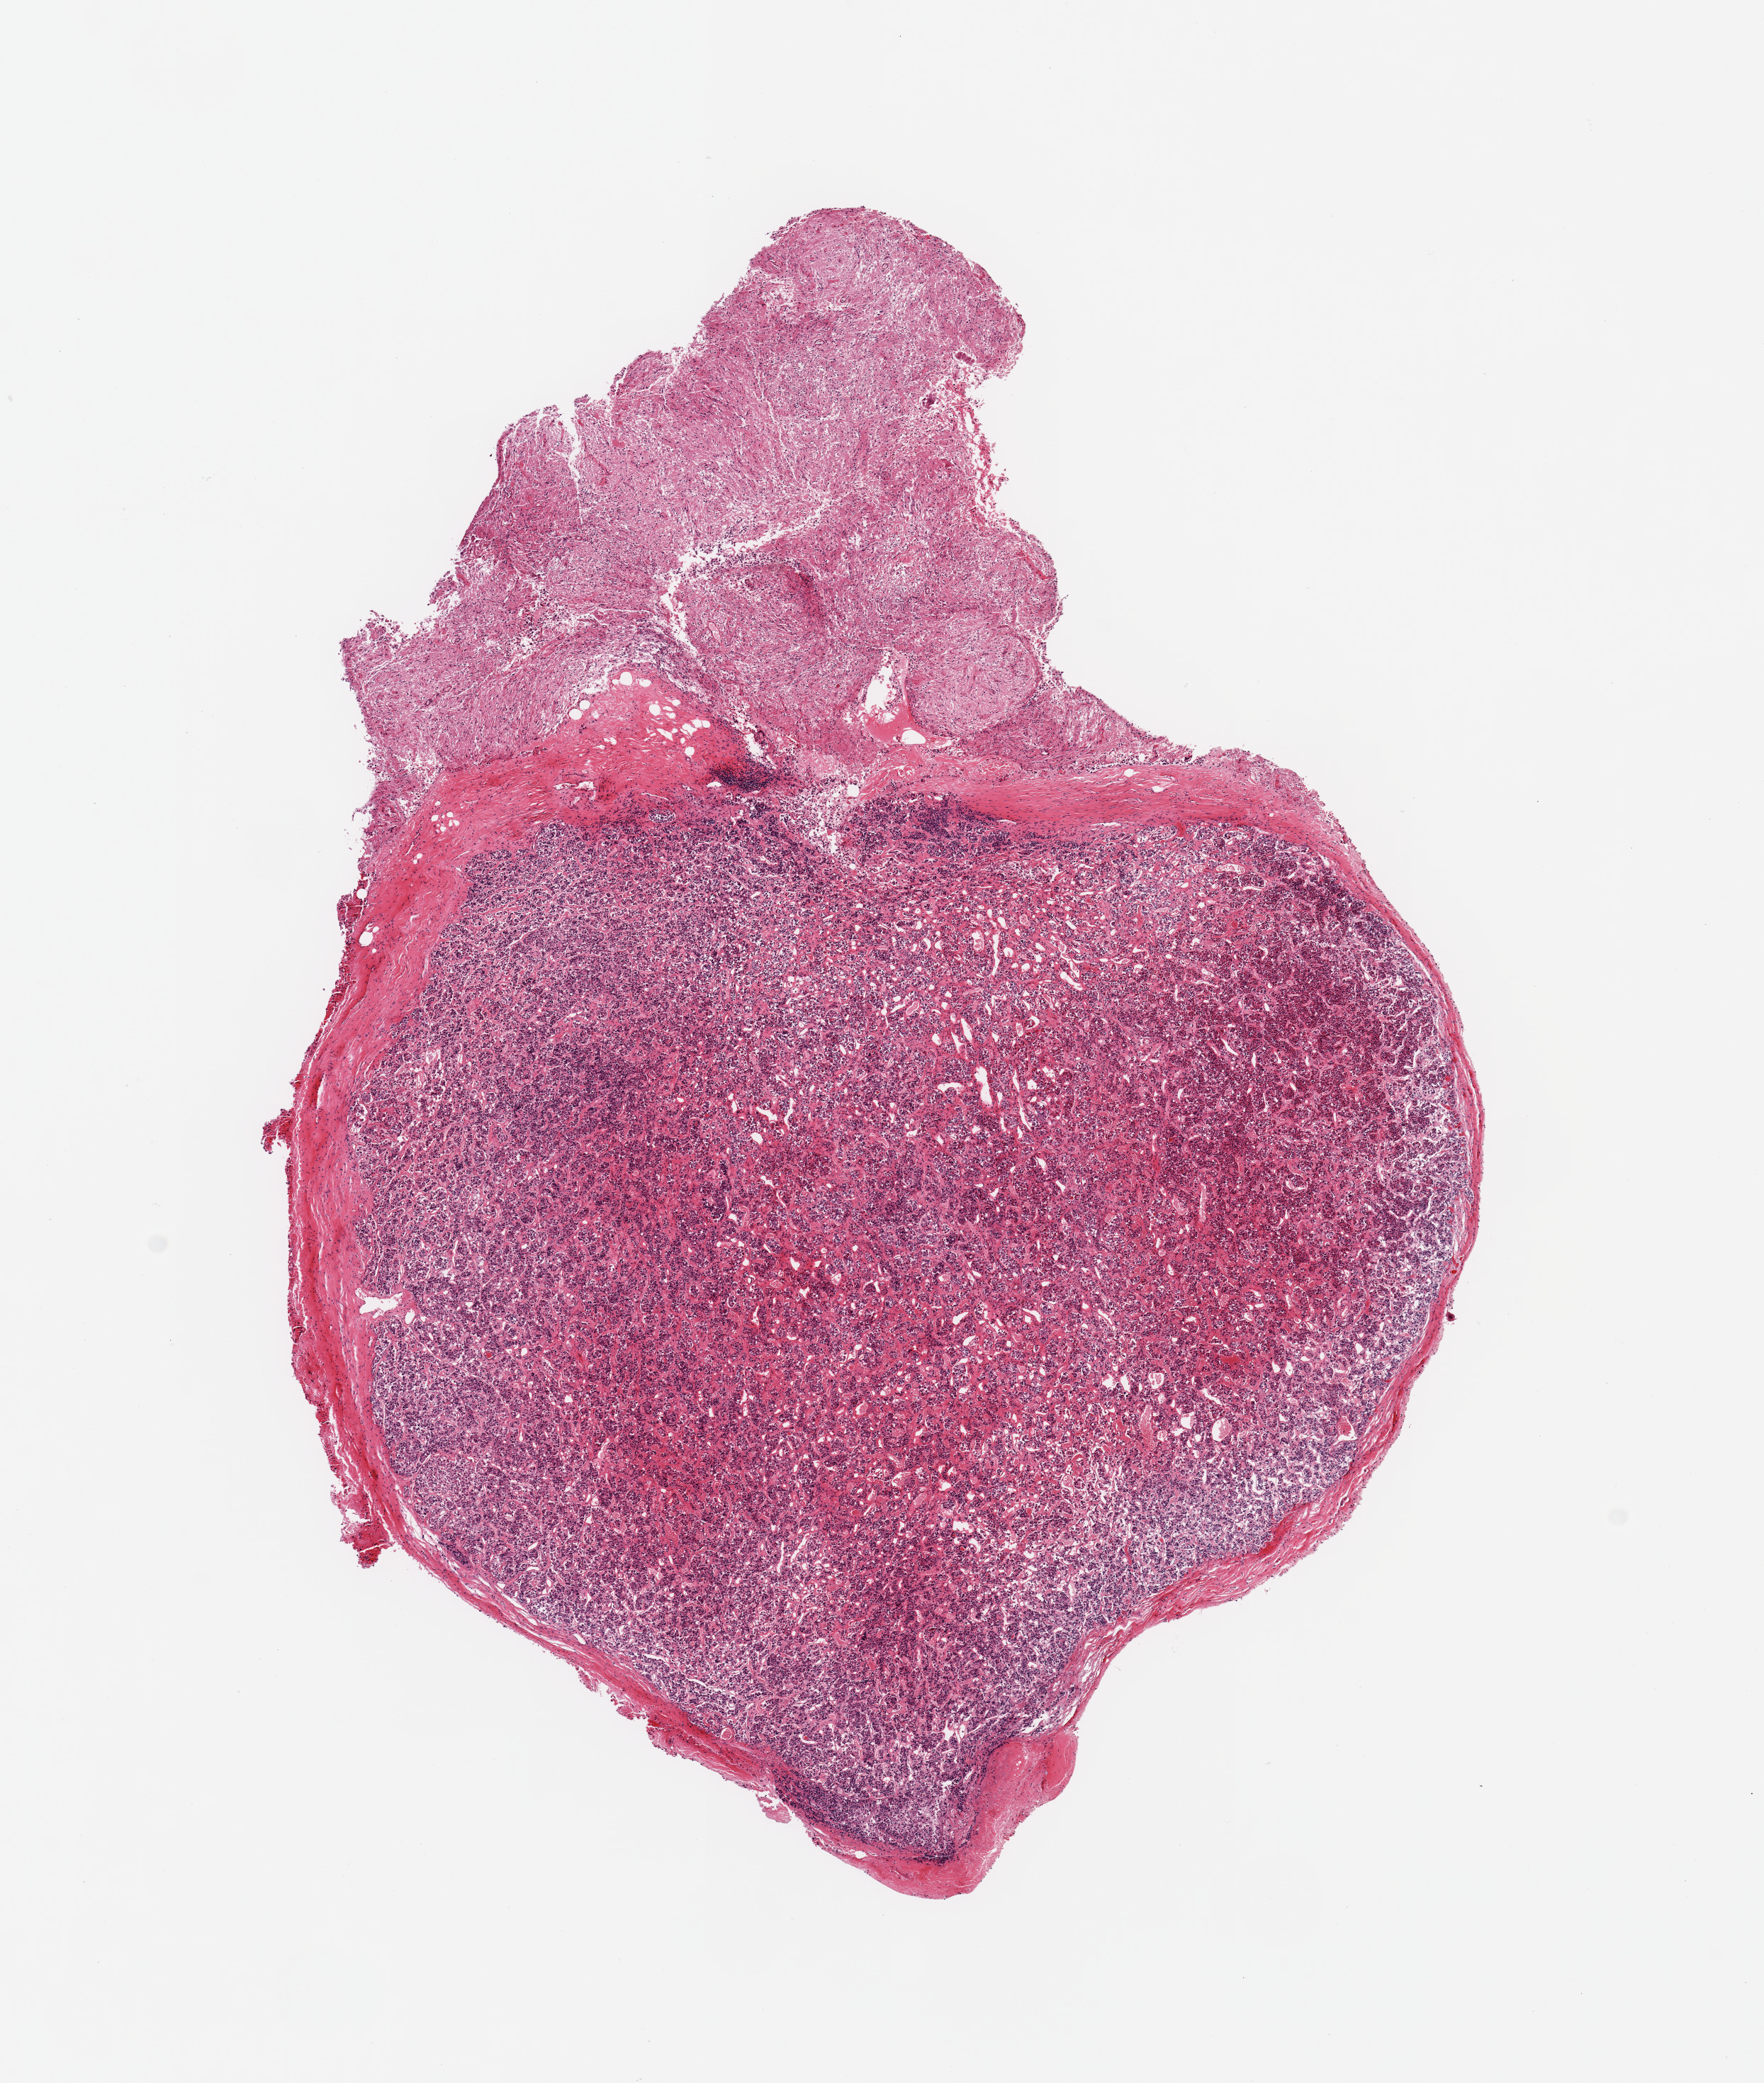
Digitized hematoxylin and eosin (H&E)-stained section, shown as a low-resolution overview of the whole scanned area (about 9.8 x 11.6 mm, slide scanned at 20x); PAXgene-fixed, paraffin-embedded tissue; sampled site (target tissue): pituitary; donor tissue sample. Male donor.
Pathologist's review note for this sample: 1 pieces; adenohypophysis and neurohypophysis.